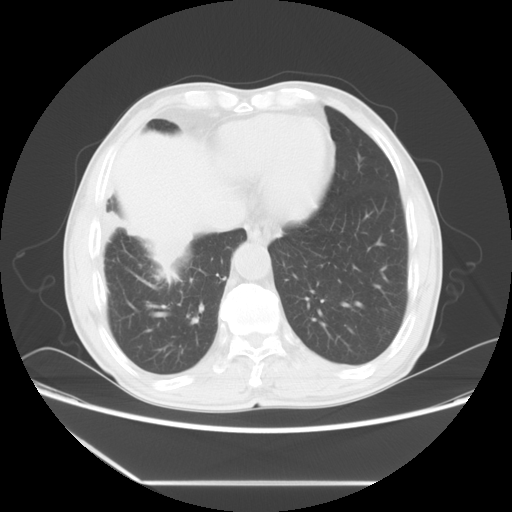
Chest CT, one axial slice; position 18 of 60 along the scan axis; reconstruction kernel STANDARD; 120 kVp; lung window (W 1500 / L -600 HU); 5 mm slice thickness; 512 × 512 image matrix. Patient: male, 72 years. From the clinical record (not read from this slice): clinical TNM (as recorded): T1c N0 M0.
Structures marked on this image (rectangle marked by the reading radiologist):
- lung tumour (recorded histology: squamous cell carcinoma): bounding box [x1, y1, x2, y2] px = [105, 209, 194, 285]